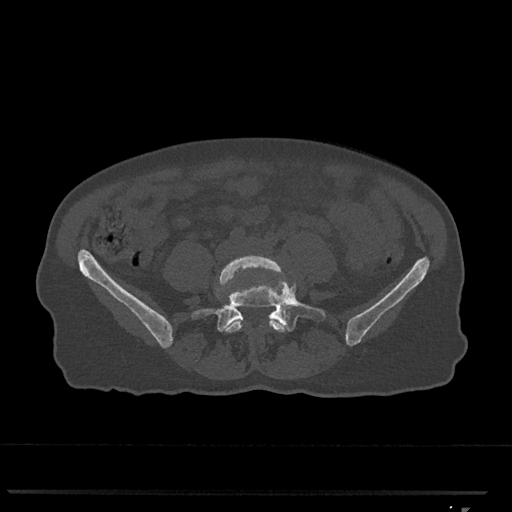
CT including the spine, one axial slice; slice 172 of 793 in the series (ordered by position); reconstruction kernel Br40s/3; 120 kVp; bone window (W 1800 / L 400 HU); 512 × 512 image matrix, field of view 380 × 380 mm. Patient: female, 62 years. From the clinical record (not read from this slice): primary cancer: renal.
Annotated regions visible in this slice (semi-automatic segmentation, software-assisted and operator-edited):
- L4 vertebra: bounding box [x1, y1, x2, y2] px = [218, 255, 287, 333]
- L5 vertebra: [192, 260, 326, 333]